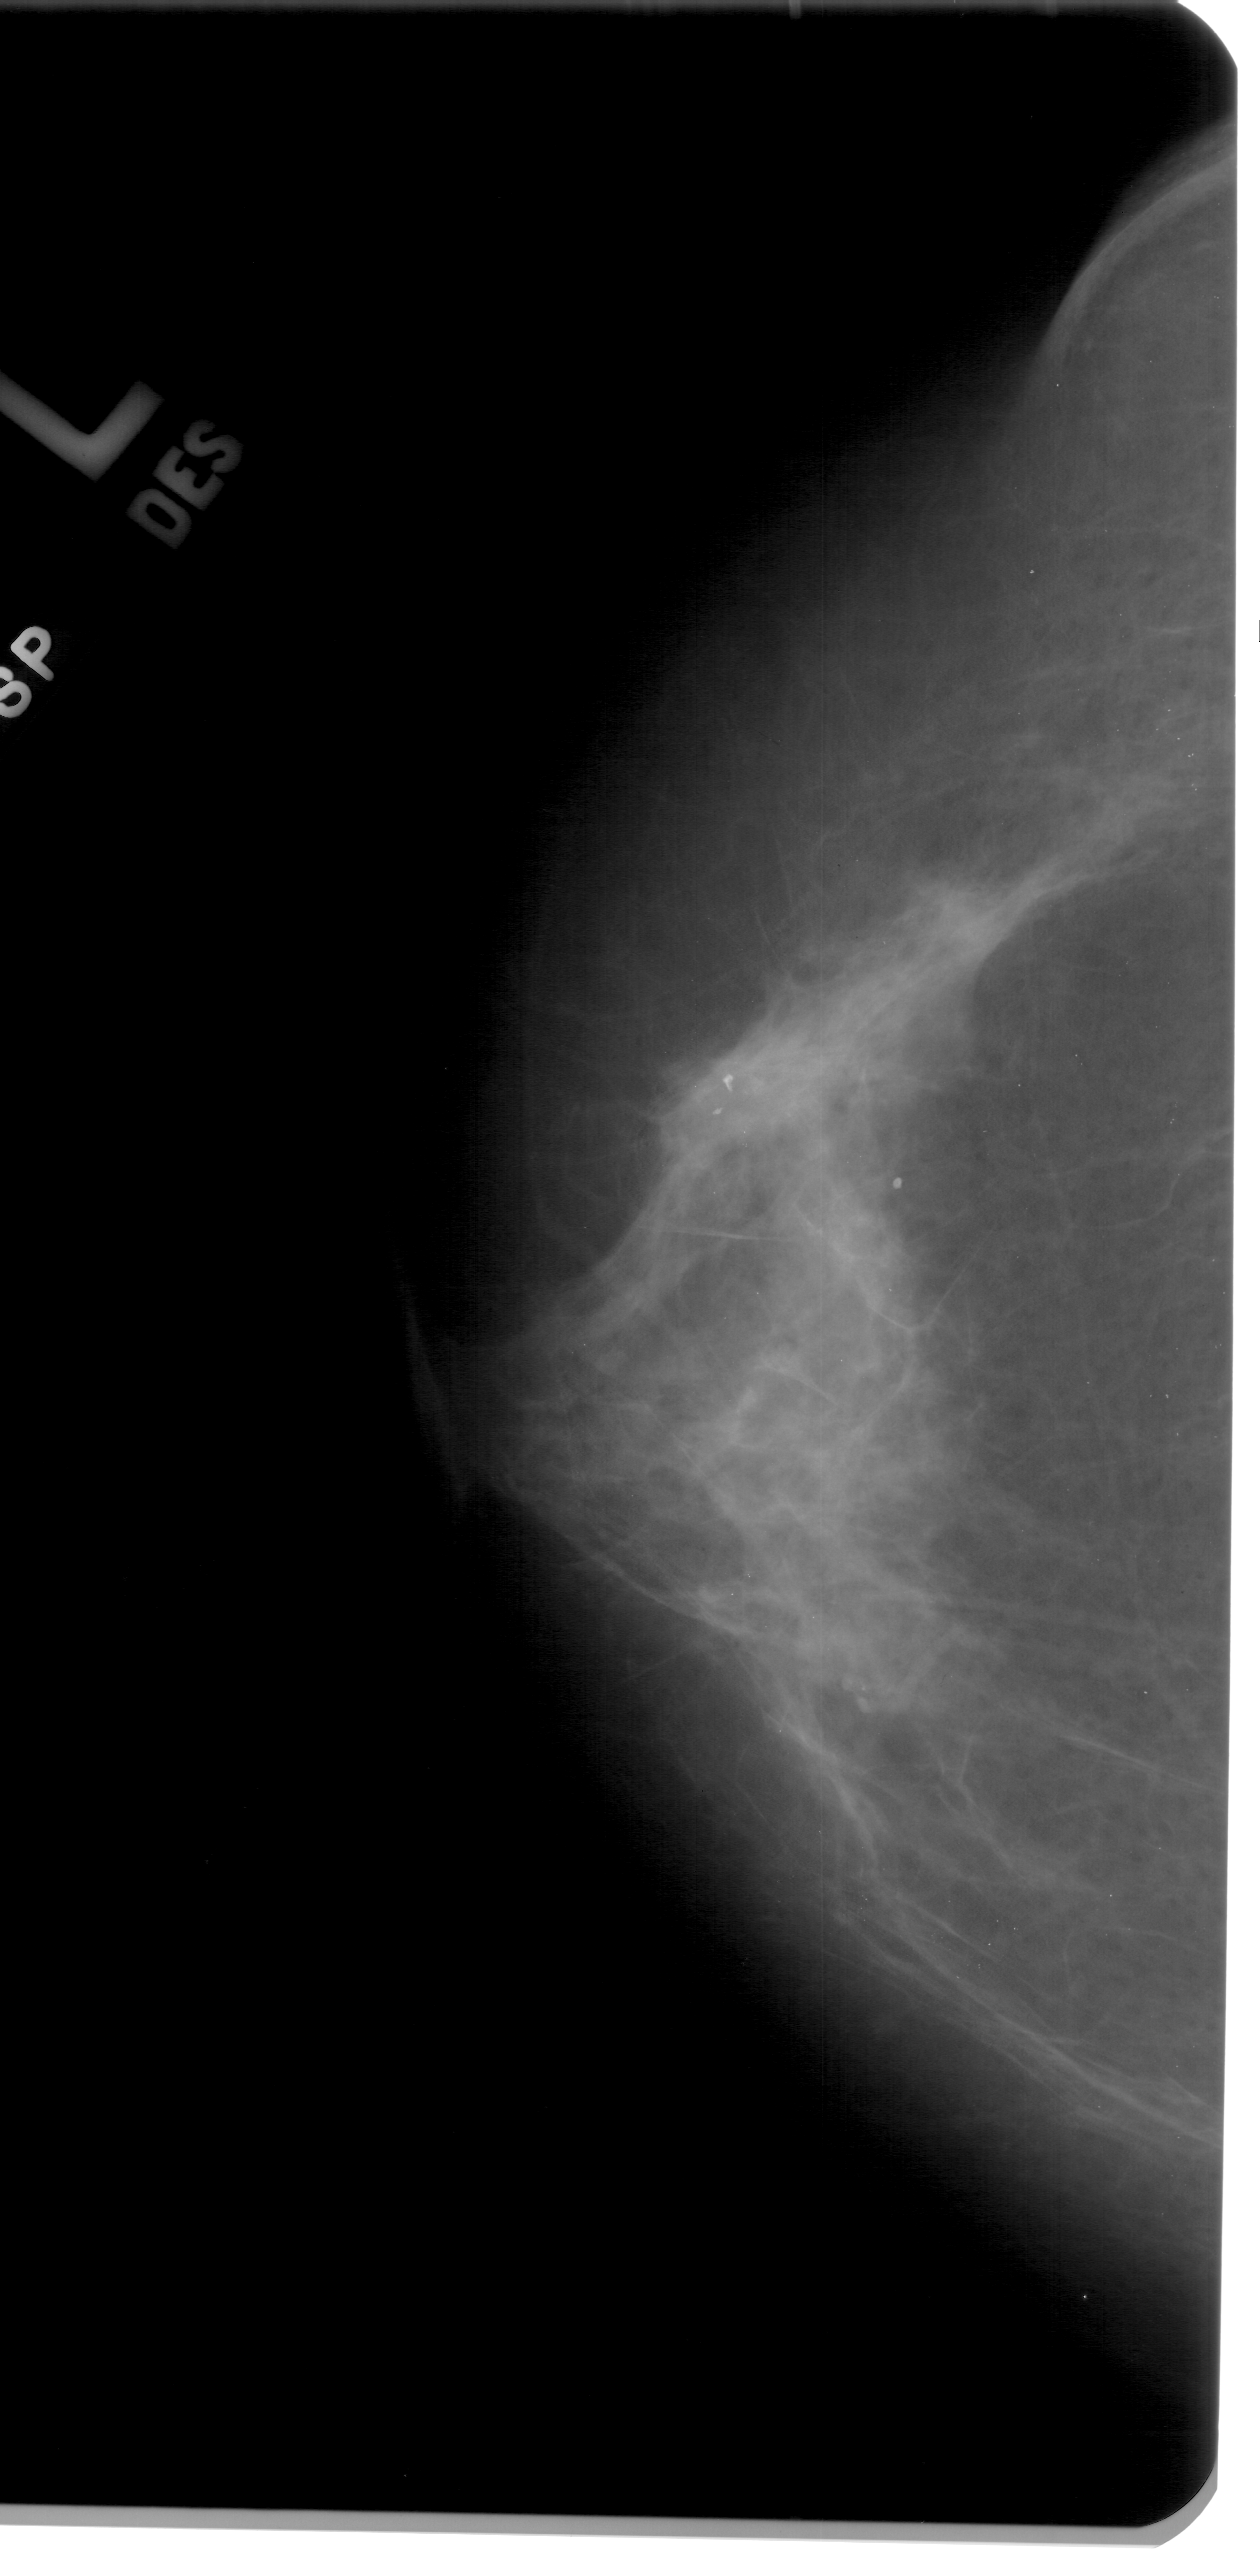
Scanned film-screen mammogram, left breast, craniocaudal (CC) view, breast composition: heterogeneously dense (BI-RADS density category 3 of 4).
- Abnormality record for this image: mass, shape irregular, margins spiculated; BI-RADS assessment category 4; pathology result (as recorded, not read from the image): malignant.